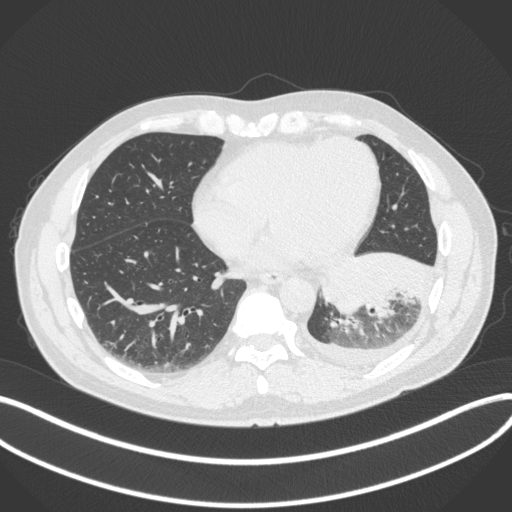
Chest CT, one axial slice; position 121 of 350 along the scan axis; 120 kVp; lung window (W 1500 / L -600 HU); 1 mm slice thickness; 512 × 512 image matrix, field of view 400 × 400 mm. Patient: male, 58 years. Case-level facts recorded for this patient, not image findings: clinical TNM (as recorded): T3 N1 M1b.
Annotated regions visible in this slice (bounding box drawn by a radiologist):
- lung tumour (recorded histology: small cell carcinoma): bounding box (x1, y1, x2, y2) in pixels: (318, 246, 440, 318)